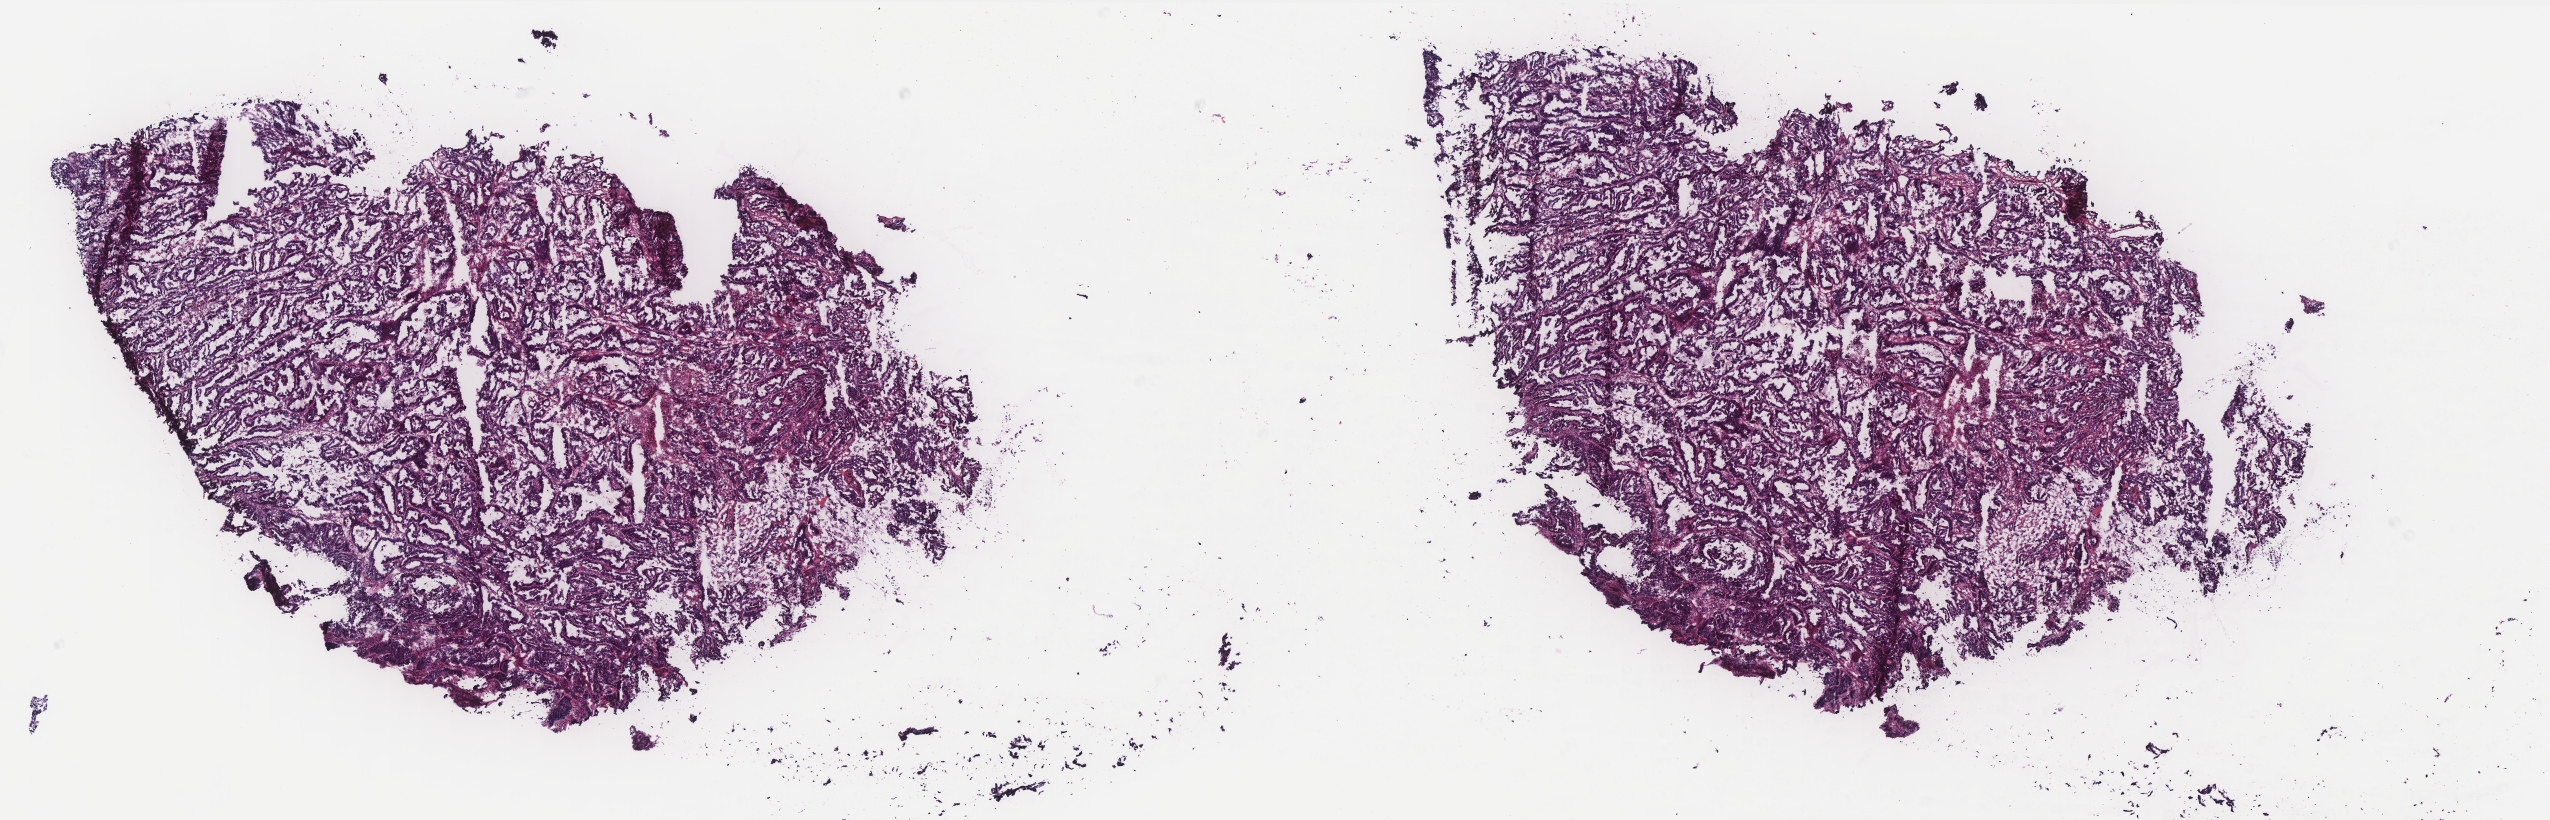
Digitized Hematoxylin and eosin (H&E) stained tissue section (whole slide), whole scanned area (about 20.4 x 6.6 mm, from a 40x scan) shown as a low-resolution overview. Frozen section from the bottom of the tissue portion. Primary tumour sample from the uterus. Female patient; age at initial diagnosis 67 years. Histologic grade: G3 (poorly differentiated). Slide review estimates, as recorded: tumour cells 60%, tumour nuclei 80%, normal cells 0%, stromal cells 20%, necrosis 20%. Infiltration values recorded for this section: lymphocyte infiltration 10%, monocyte infiltration 10%, neutrophil infiltration 20%.
• FIGO stage: IIIA
• diagnosis: Serous cystadenocarcinoma, NOS (endometrium)